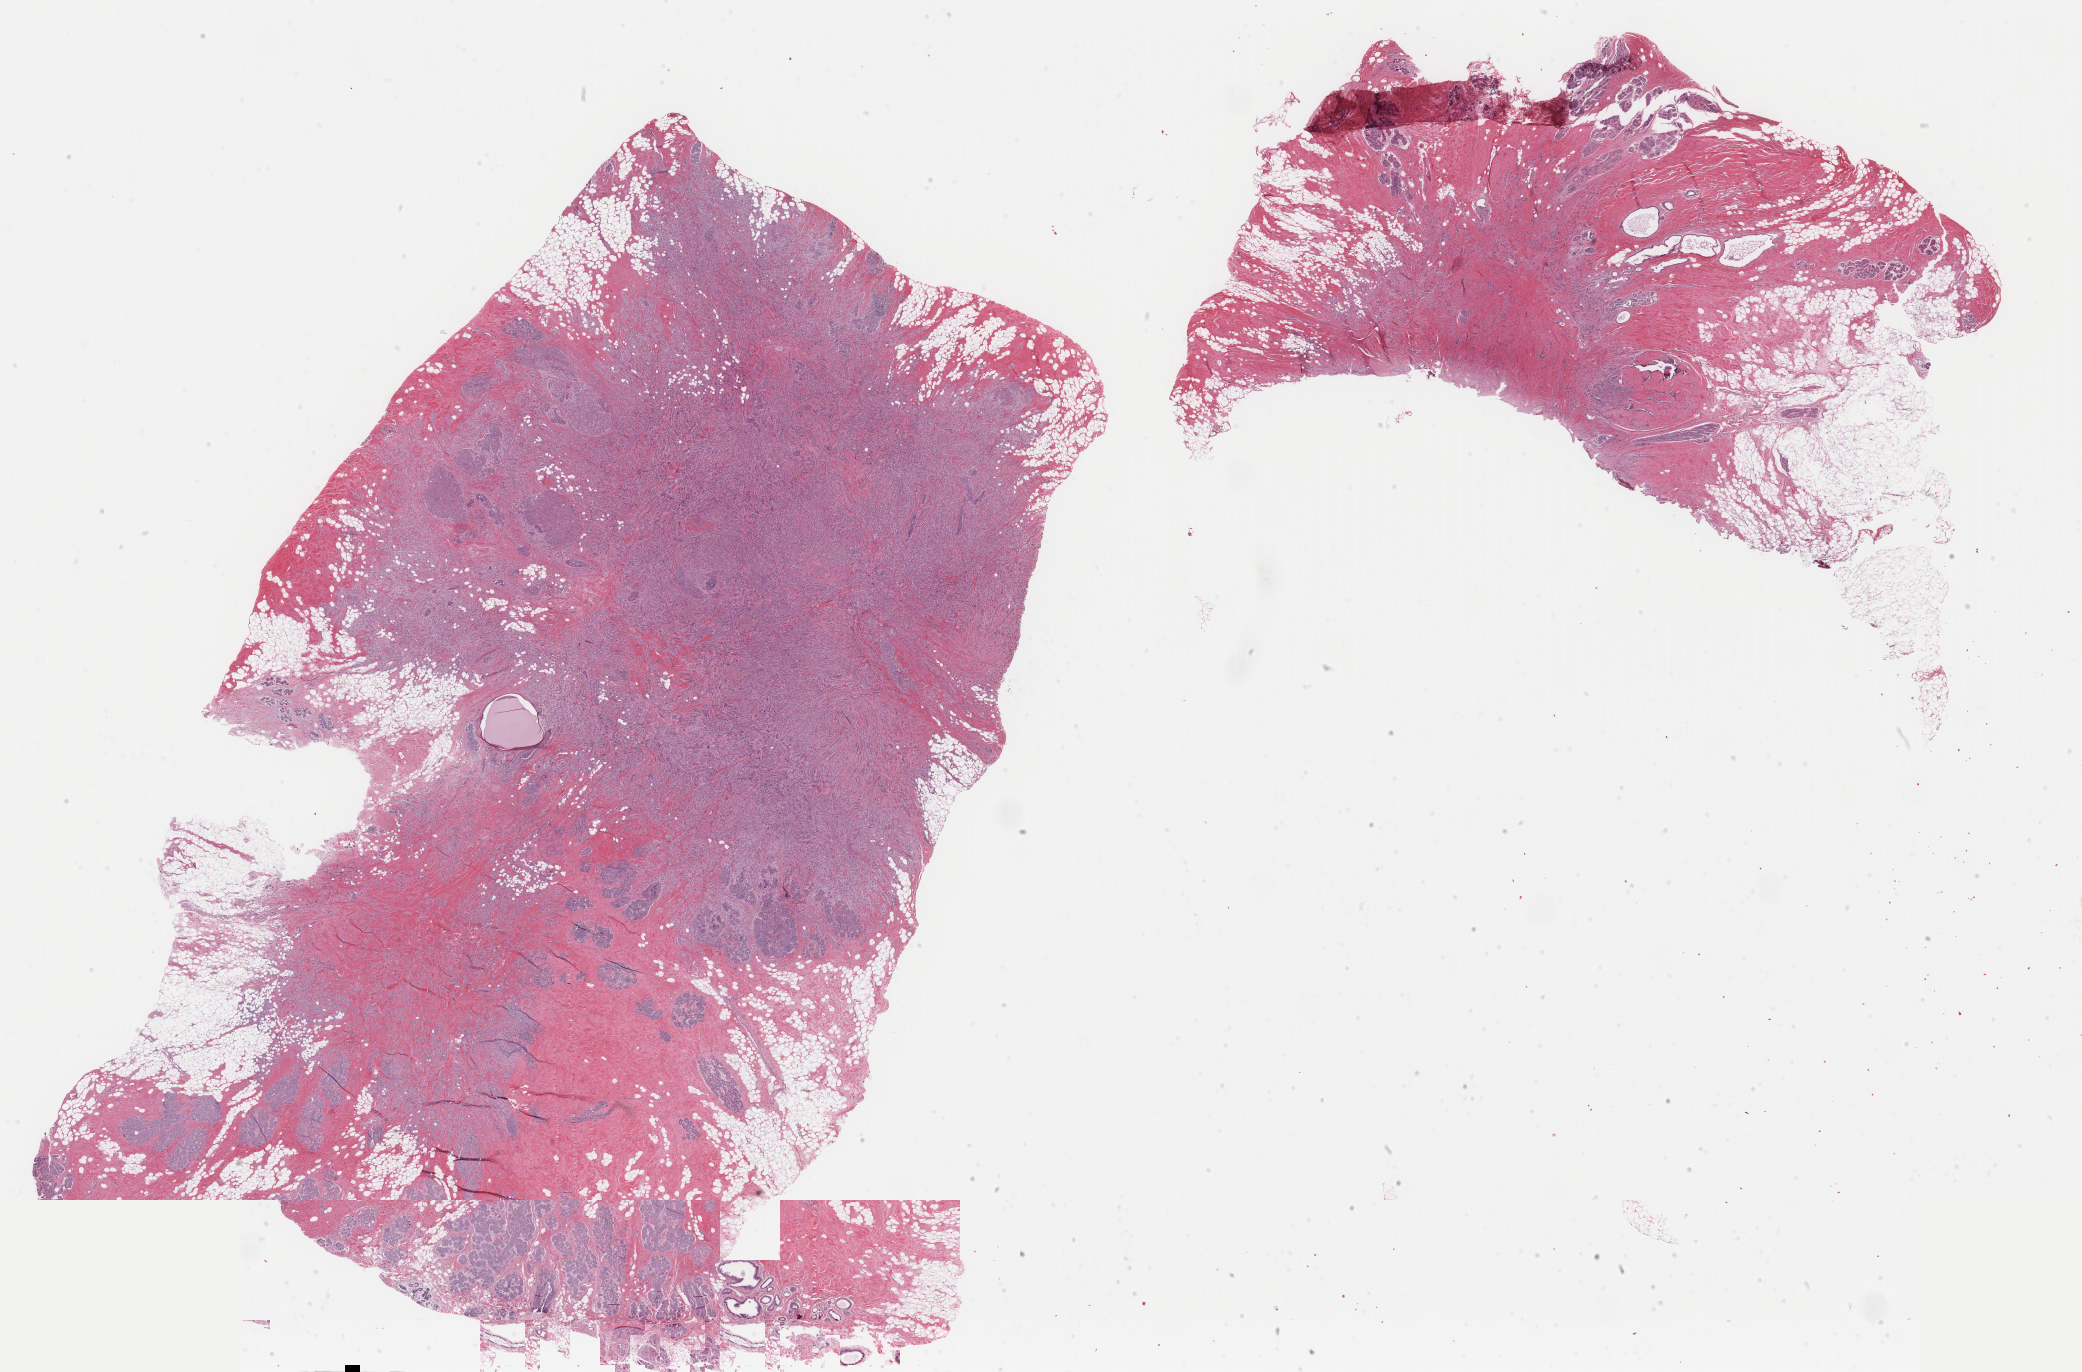
Hematoxylin and eosin (H&E) stained whole-slide image, a low-resolution overview of the entire scanned area, about 33.1 x 21.8 mm (slide scanned at 40x), formalin-fixed paraffin-embedded (FFPE) diagnostic section, sample: primary tumour, breast. Female, age 49 years at initial diagnosis.
• histologic diagnosis: Lobular carcinoma, NOS
• TNM: T1 N1 M0
• AJCC pathologic stage: II (6th edition)
• lymph nodes positive (case pathology): 1 of 3 examined